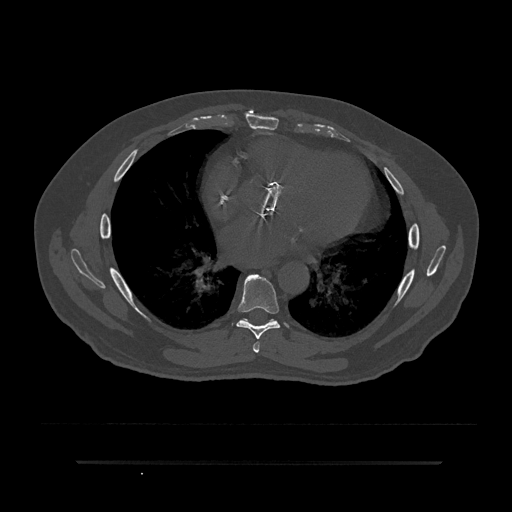
CT including the spine, one axial slice; position 472 of 797 along the scan axis; reconstruction kernel Br40s/3; bone window (W 1800 / L 400 HU); 0.5 mm slice thickness; 512 × 512 image matrix, field of view 464 × 464 mm. Male patient, age 59 years. From the clinical record (not read from this slice): primary cancer: bile ducts.
Outlined on this slice (semi-automatically segmented with operator editing):
- T6 vertebra: bounding box (x1, y1, x2, y2) in pixels: (253, 342, 260, 353)
- T7 vertebra: (236, 274, 280, 339)
- T8 vertebra: (241, 318, 248, 322)